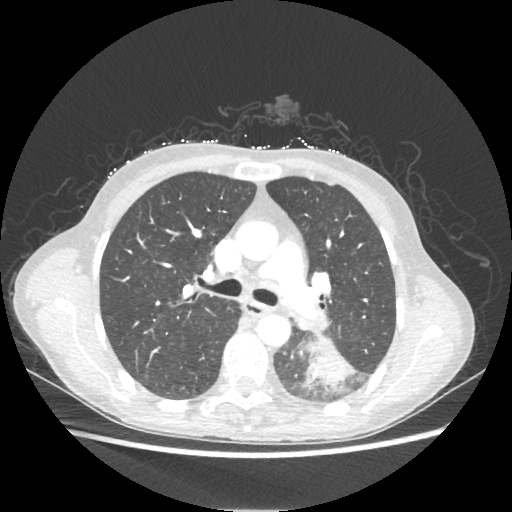
Chest CT, one axial slice. Slice 138 of 221 in the series (ordered by position). Reconstruction kernel STANDARD. 80 kVp. Lung window (W 1500 / L -600 HU). 1.25 mm slice thickness. 512 × 512 image matrix, field of view 360 × 360 mm. Patient: female, 53 years. Case-level facts recorded for this patient, not image findings: clinical TNM (as recorded): T3 N0 M0.
Annotated regions visible in this slice (bounding box drawn by a radiologist):
- lung tumour (recorded histology: adenocarcinoma): bounding box <305,339,353,386> (left, top, right, bottom; pixels)